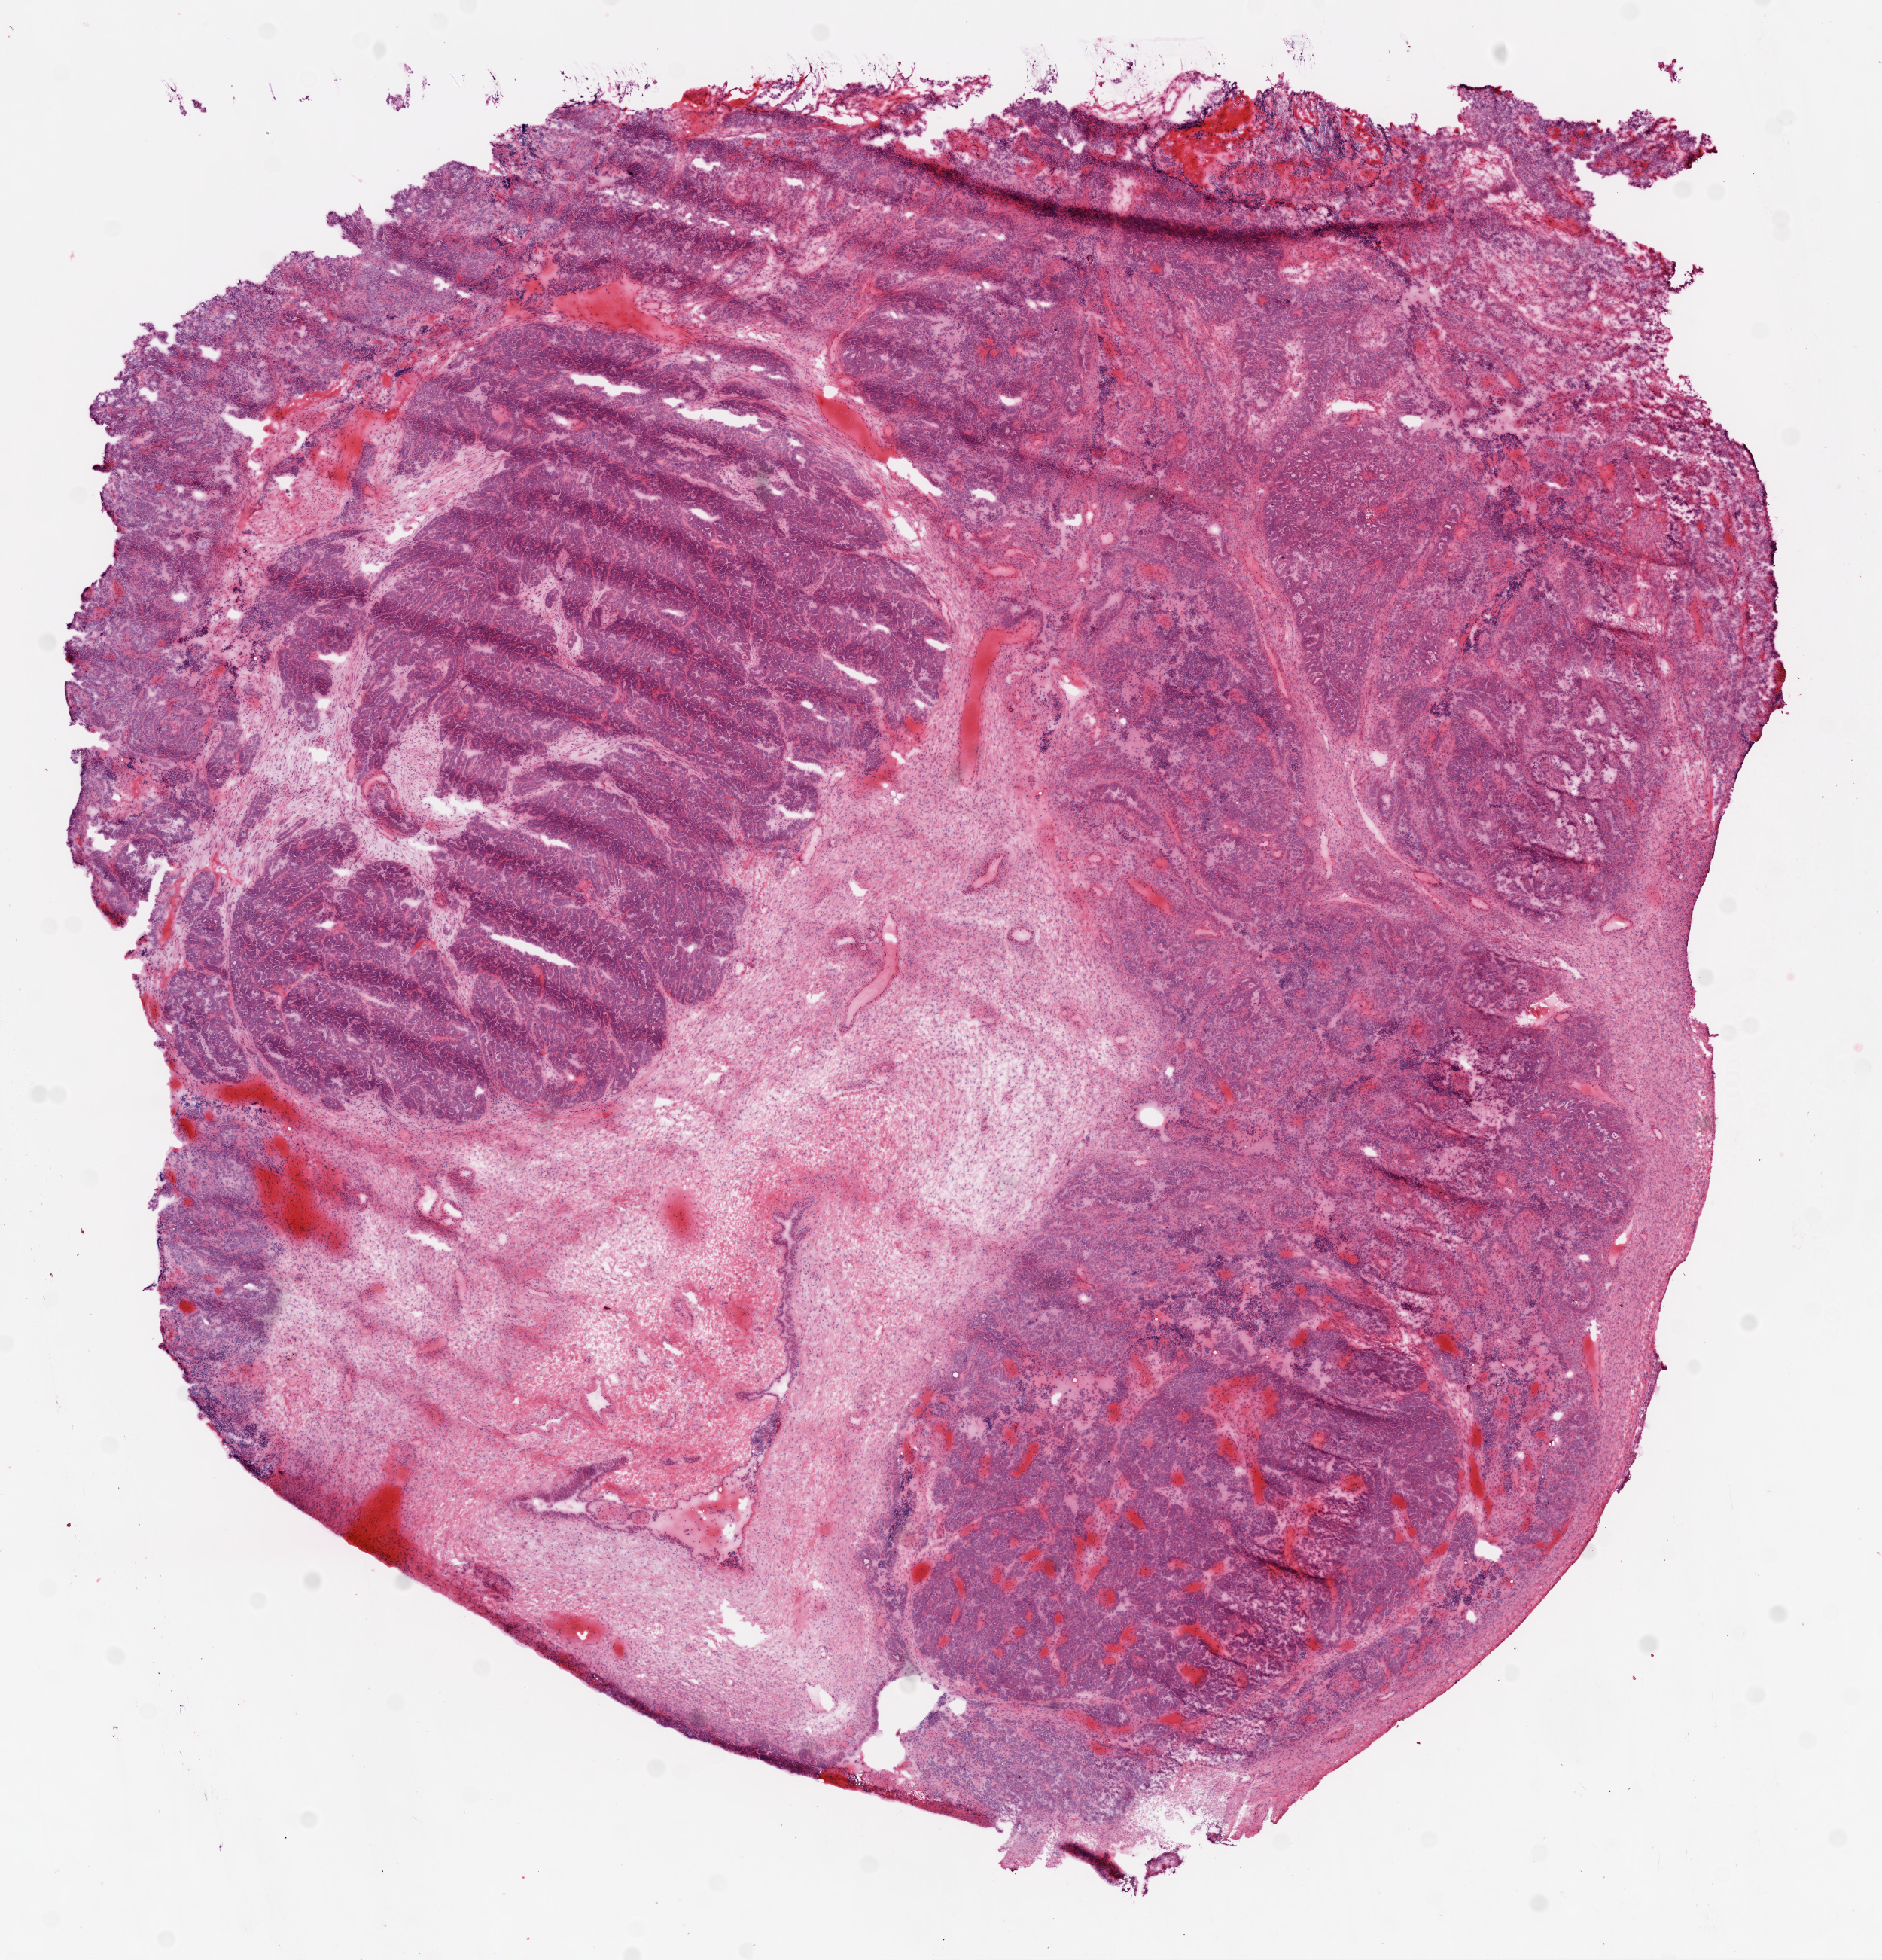
H&E-stained whole-slide image, shown as a low-resolution overview of the whole scanned area (about 10.0 x 10.4 mm, acquisition: 20x scan). Frozen section from the top of the tissue portion. Primary tumour sample from the ovary. Patient: female, age at initial diagnosis 71 years. Histologic grade: G3 (poorly differentiated). Composition of this section per pathologist review: tumour cells 90%, tumour nuclei 90%, normal cells 0%, stromal cells 10%, necrosis 0%.
* FIGO stage: IIIC
* laterality: bilateral
* pathologic diagnosis: Serous cystadenocarcinoma, NOS